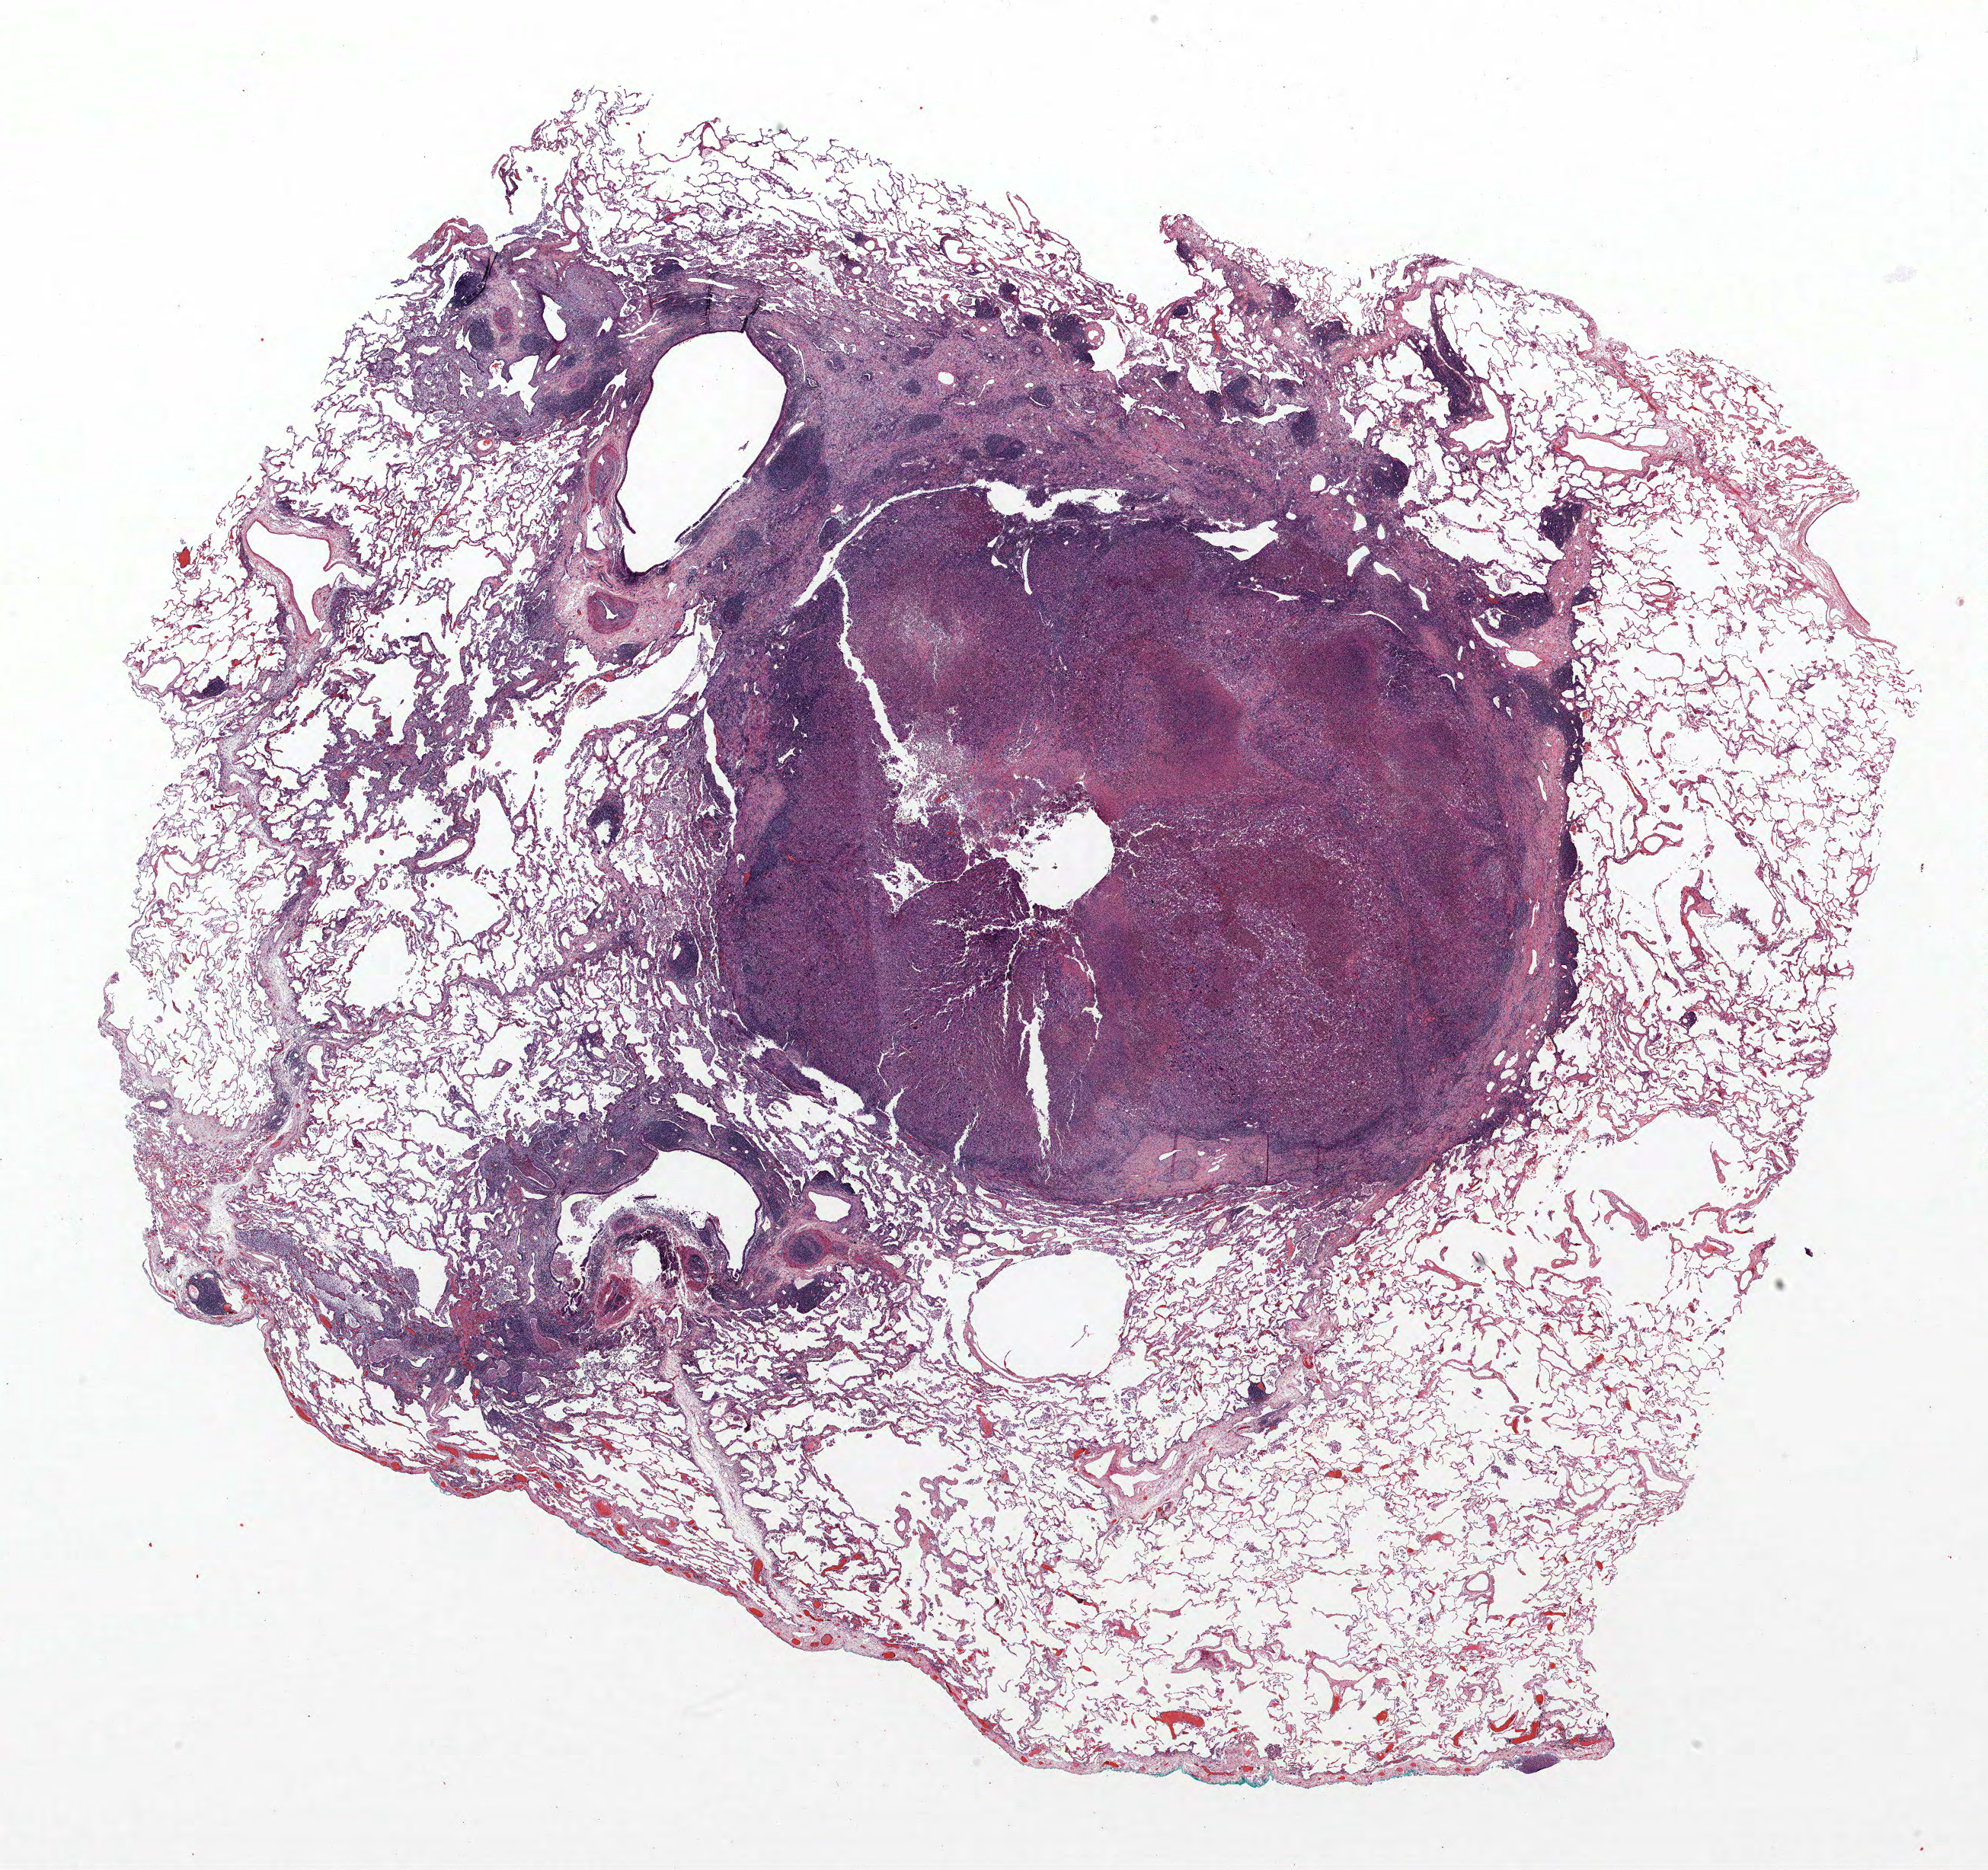
Whole-slide histology image, H&E — shown as a low-resolution overview of the whole scanned area (about 20.9 x 19.6 mm); FFPE section; lung tissue. Female, age 56 at enrolment. Current smoker at enrolment. Grade: poorly differentiated (G3).
* participant's lung-cancer diagnosis: Adenocarcinoma, NOS
* primary tumour location (clinical record): right upper lobe
* tumour size (pathology): 20 mm
* stage (AJCC 6th edition): IA